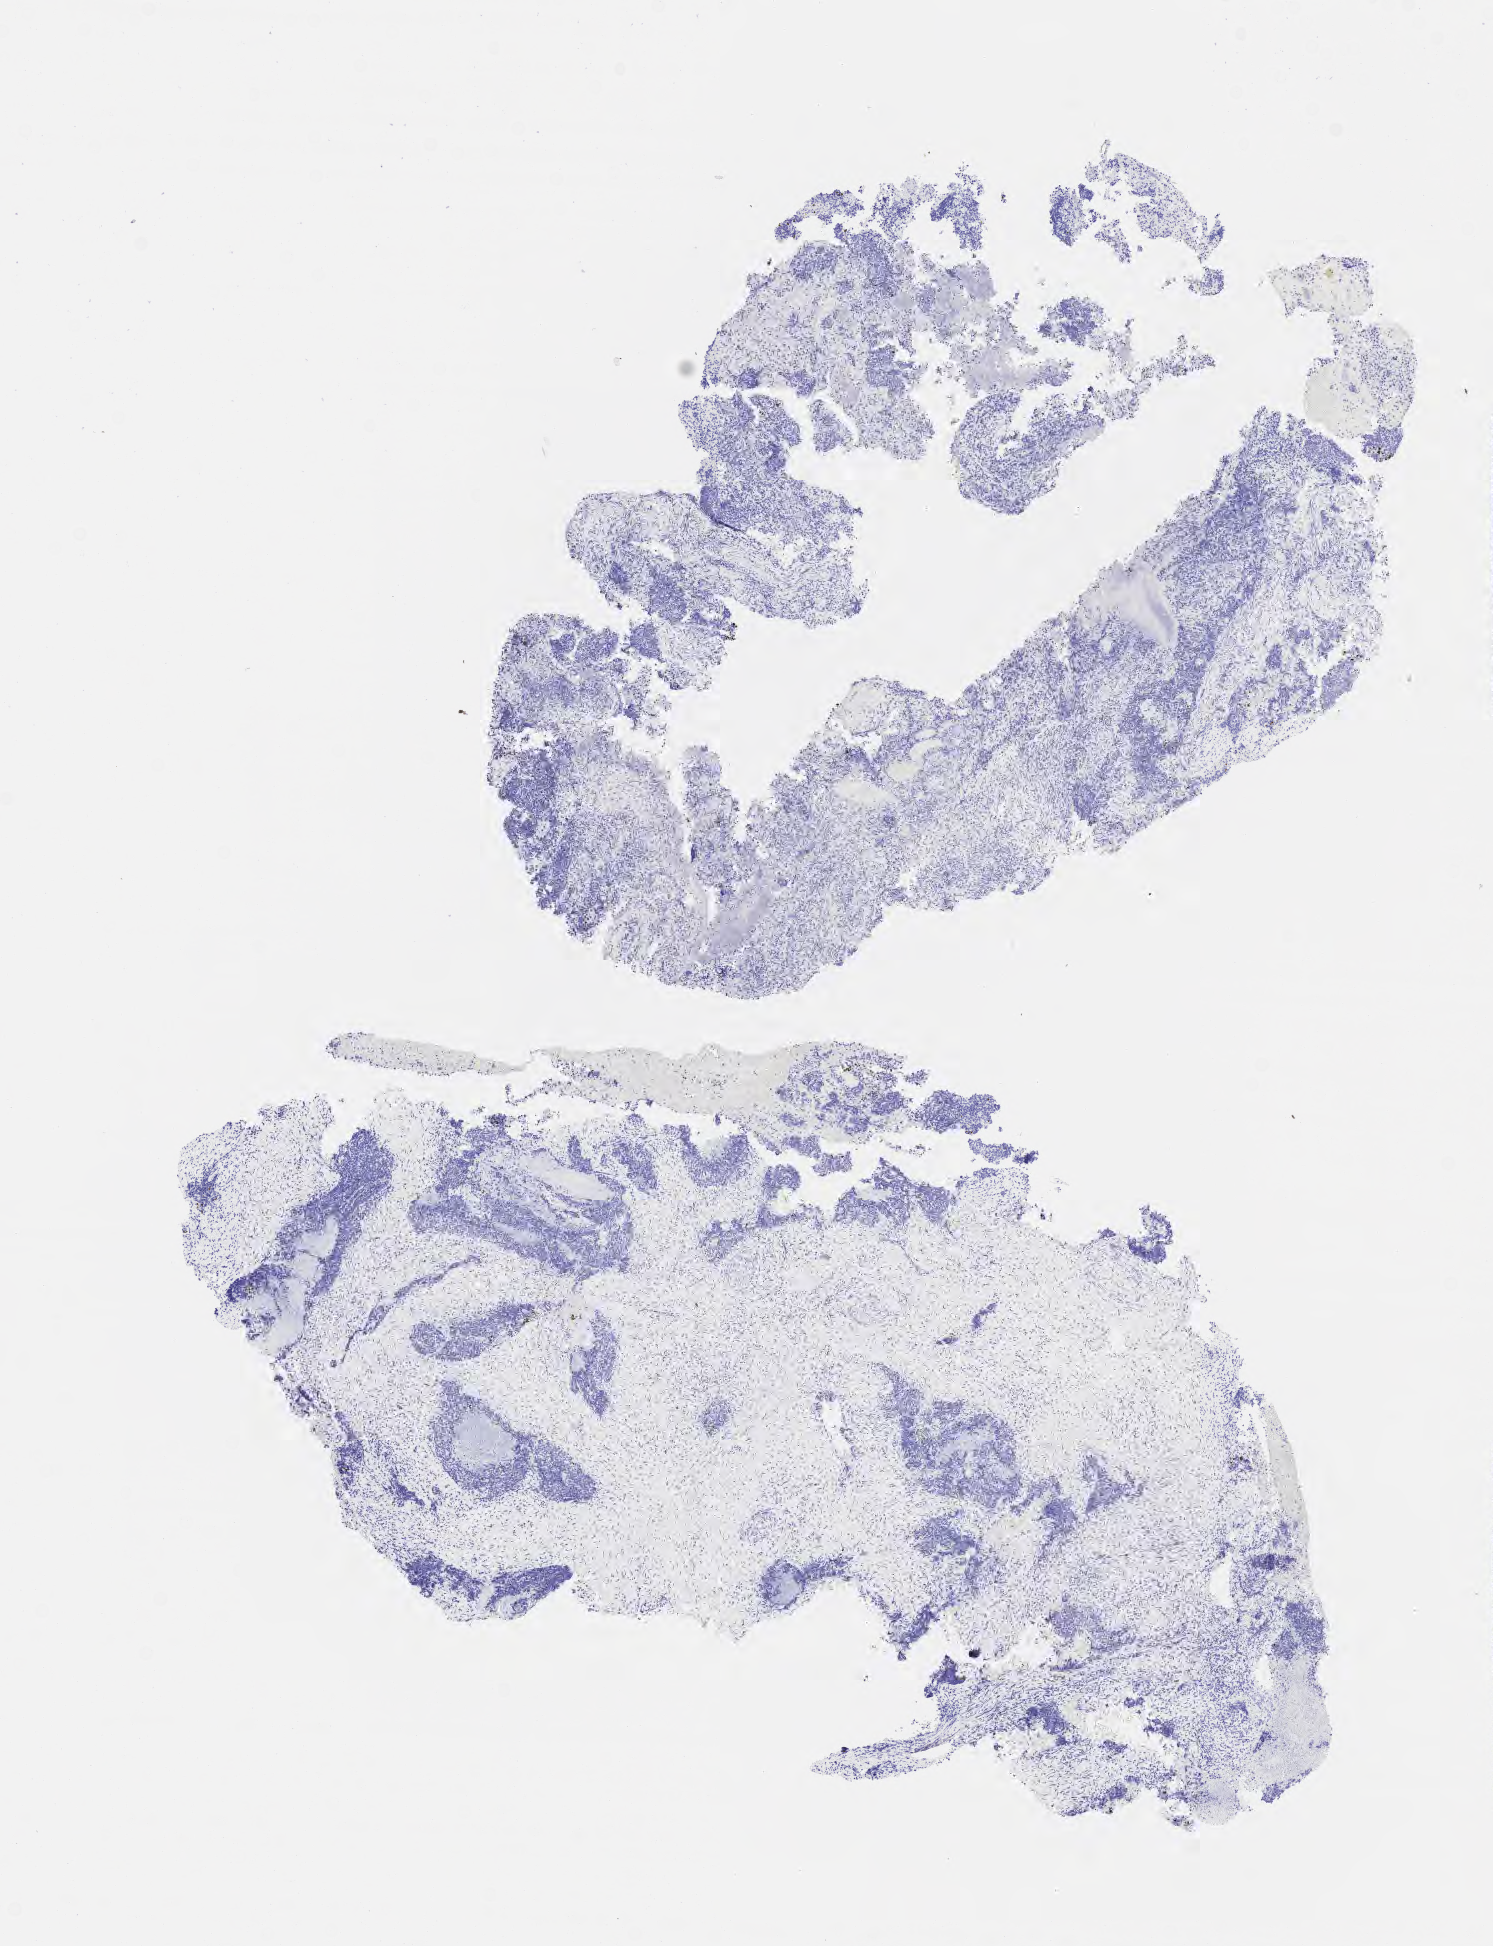
Immunohistochemistry (IHC) whole-slide image stained for p40 — shown as a low-resolution overview of the whole scanned area (about 6.0 x 7.9 mm); specimen: tumor tissue; anatomic site: cervix. Patient: female, age 47 years.
Histologic diagnosis: Squamous cell carcinoma, large cell, nonkeratinizing, NOS.